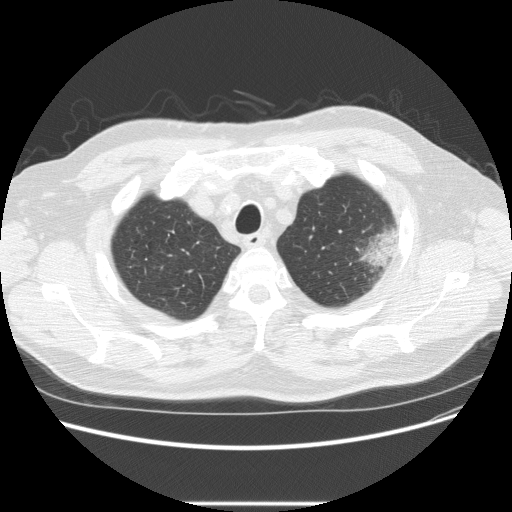
Low-dose screening chest CT, one axial slice; position 194 of 233 along the scan axis; lung window (W 1500 / L -600 HU); 512 × 512 image matrix, field of view 380 × 380 mm.
Outlined on this slice (manually delineated by an expert):
- lesion 1 (tumor, upper lobe of left lung): box from (x=359, y=232) to (x=397, y=269) px